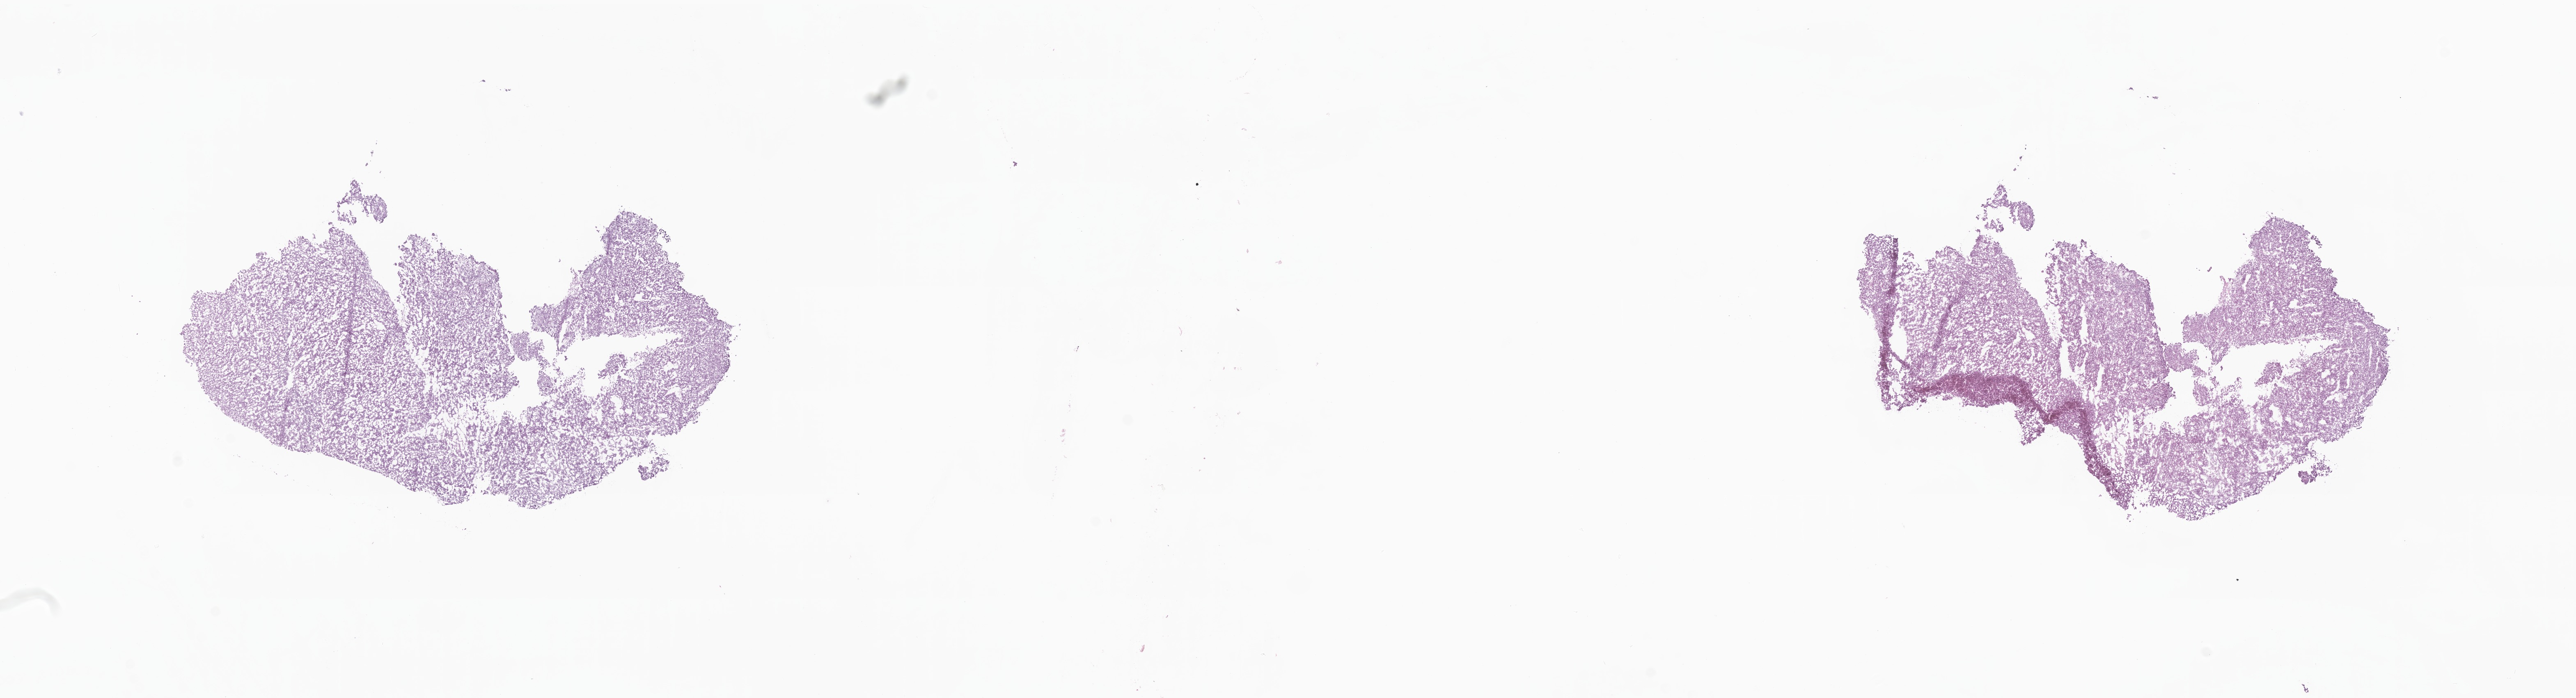
H&E whole-slide image, whole scanned area (about 26.5 x 7.2 mm) shown as a low-resolution overview; cryosection; primary tumor; site: liver. Male, age 86 years at initial diagnosis. Tumor grade: G3 (poorly differentiated). Composition of this section per pathologist review: tumor cells 90%, tumor nuclei 90%, stromal cells 10%, necrosis 0%, normal cells 0%. Infiltration values recorded for this section: lymphocyte infiltration 0%, monocyte infiltration 0%, neutrophil infiltration 0%.
- section: top of the tissue portion
- AJCC pathologic stage: Stage IIIB
- histologic diagnosis: Hepatocellular carcinoma, NOS